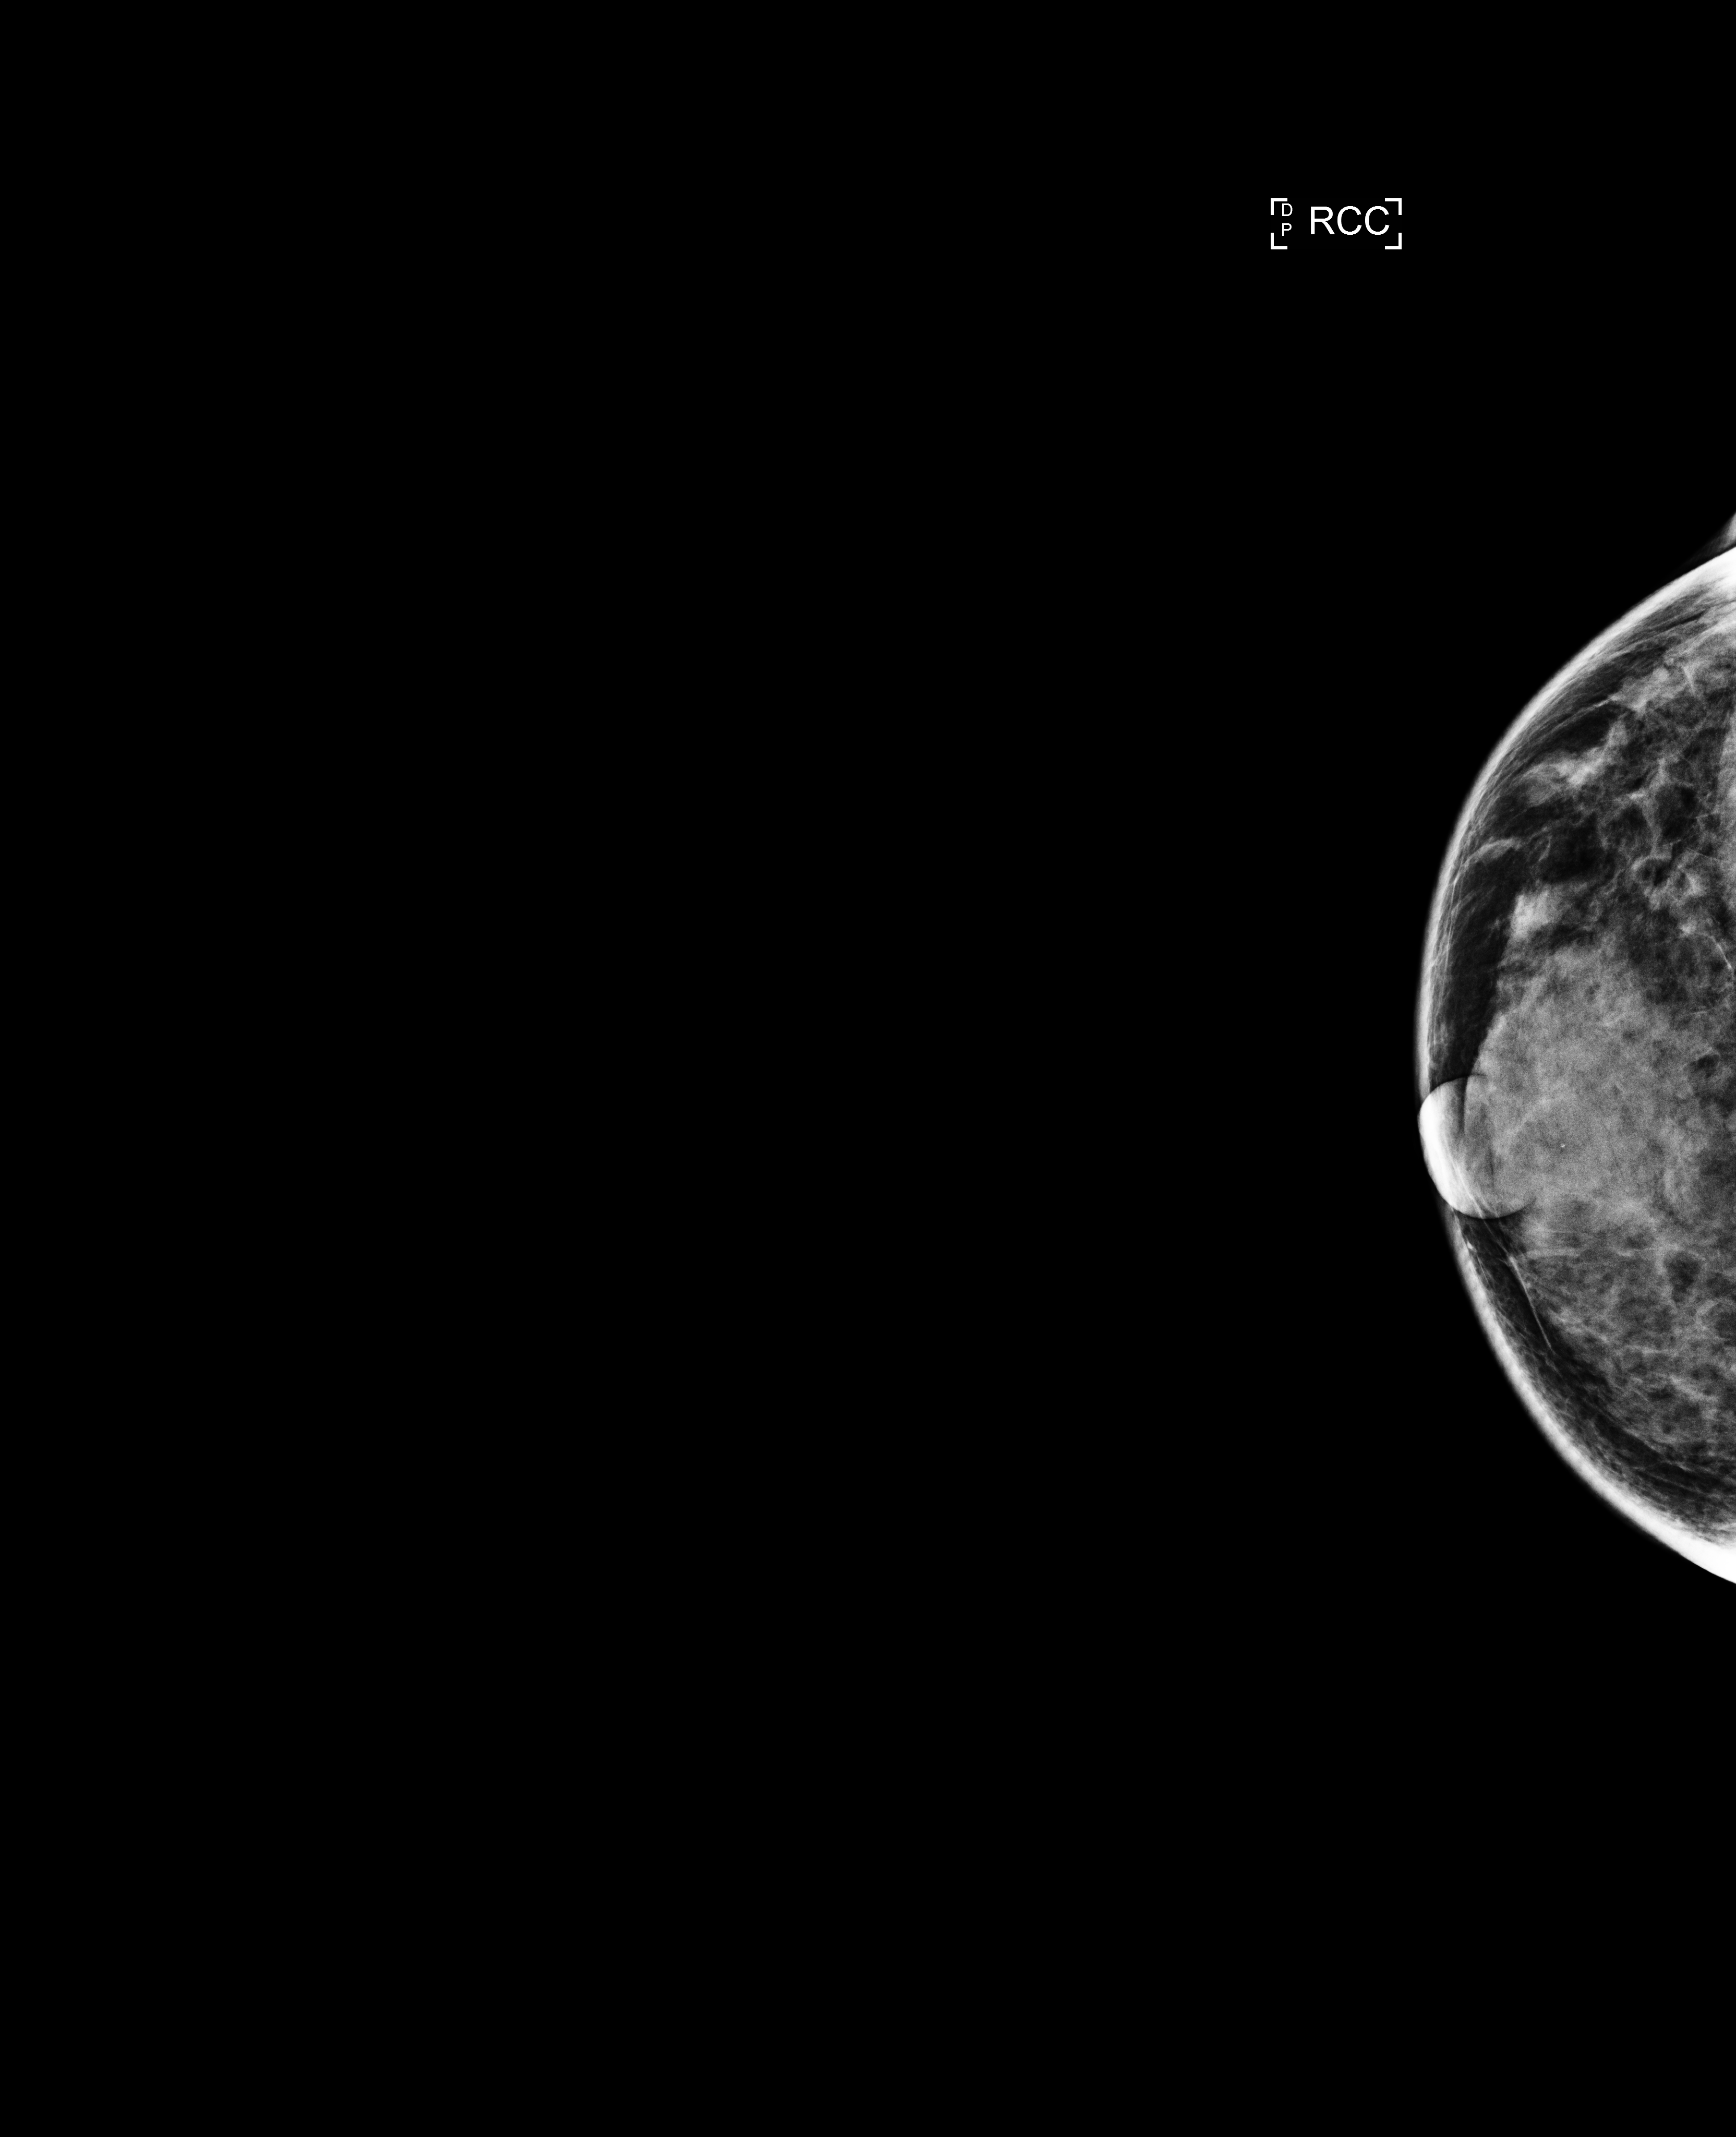
Screening examination; compressed breast thickness 36 mm; system: Selenia Dimensions. Patient: female, 60 years.
Image type: full-field digital mammogram. Breast: right. Projection: craniocaudal (CC) view.